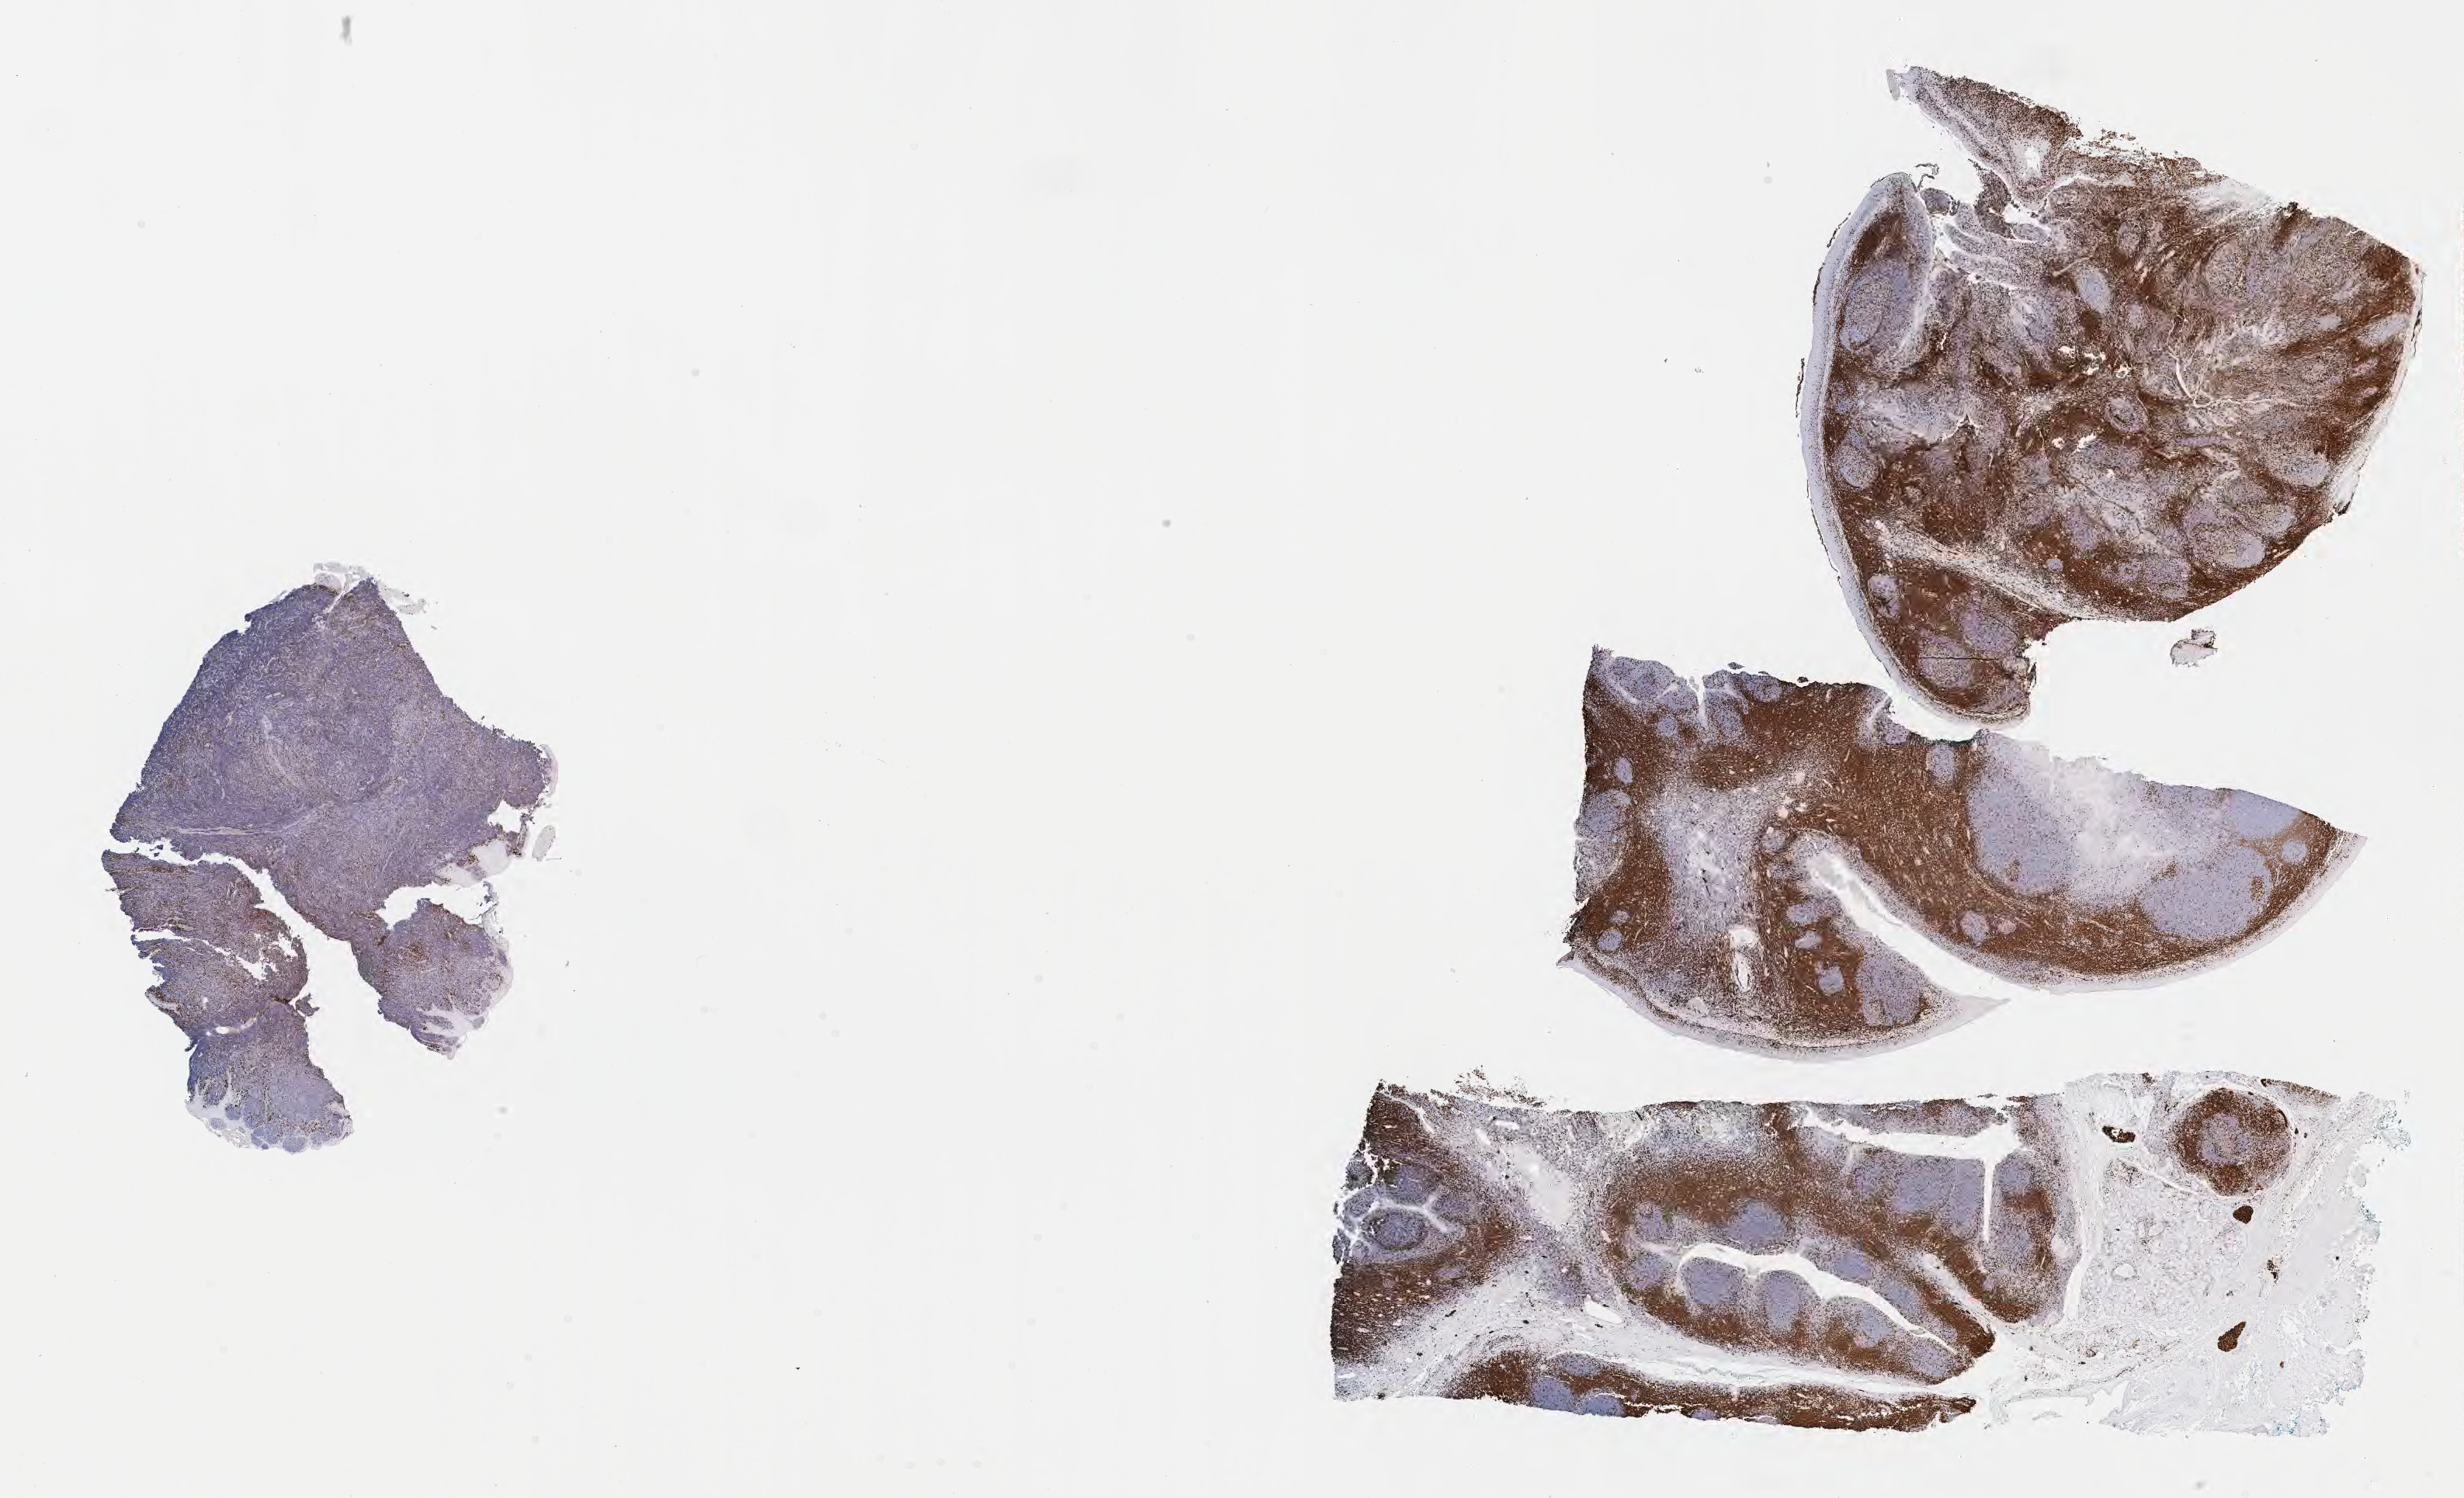
Whole-slide image, immunohistochemical stain for CD3, shown as a low-resolution overview of the whole scanned area (about 25.7 x 15.6 mm); tumor tissue; anatomic site: cranium. Male patient, aged 11.
Diagnosis: Diffuse large B-cell lymphoma, NOS.